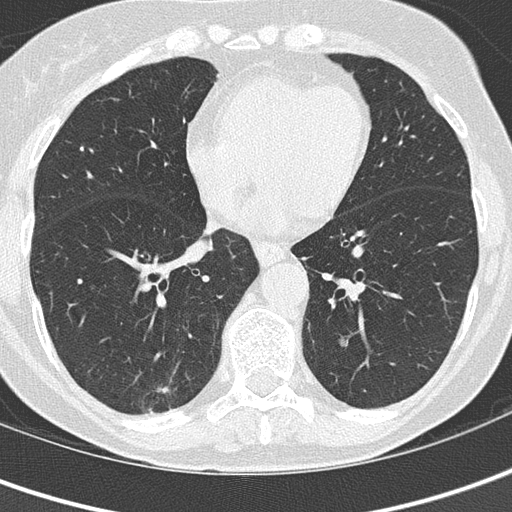
Low-dose screening chest CT, axial slice, second annual screen, lung window (W 1500 / L -600 HU), 2 mm slice thickness, lung (sharp) reconstruction kernel (B50f), 120 kVp, slice 95 of 152 in the series. Female, age 69 years at enrolment. Current smoker at enrolment.
Expert-annotated lung lesion, bounding box (x1, y1, x2, y2) in pixels: (124, 362, 186, 420). The screening reader recorded 2 non-calcified nodules or masses ≥4 mm on this exam (right lower lobe, left lower lobe); which of them this box marks is not recorded. Lung cancer was diagnosed 112 days after this screen: adenocarcinoma, NOS, right lower lobe, moderately differentiated (G2), stage IA (AJCC 6th edition), 16 mm at pathology.